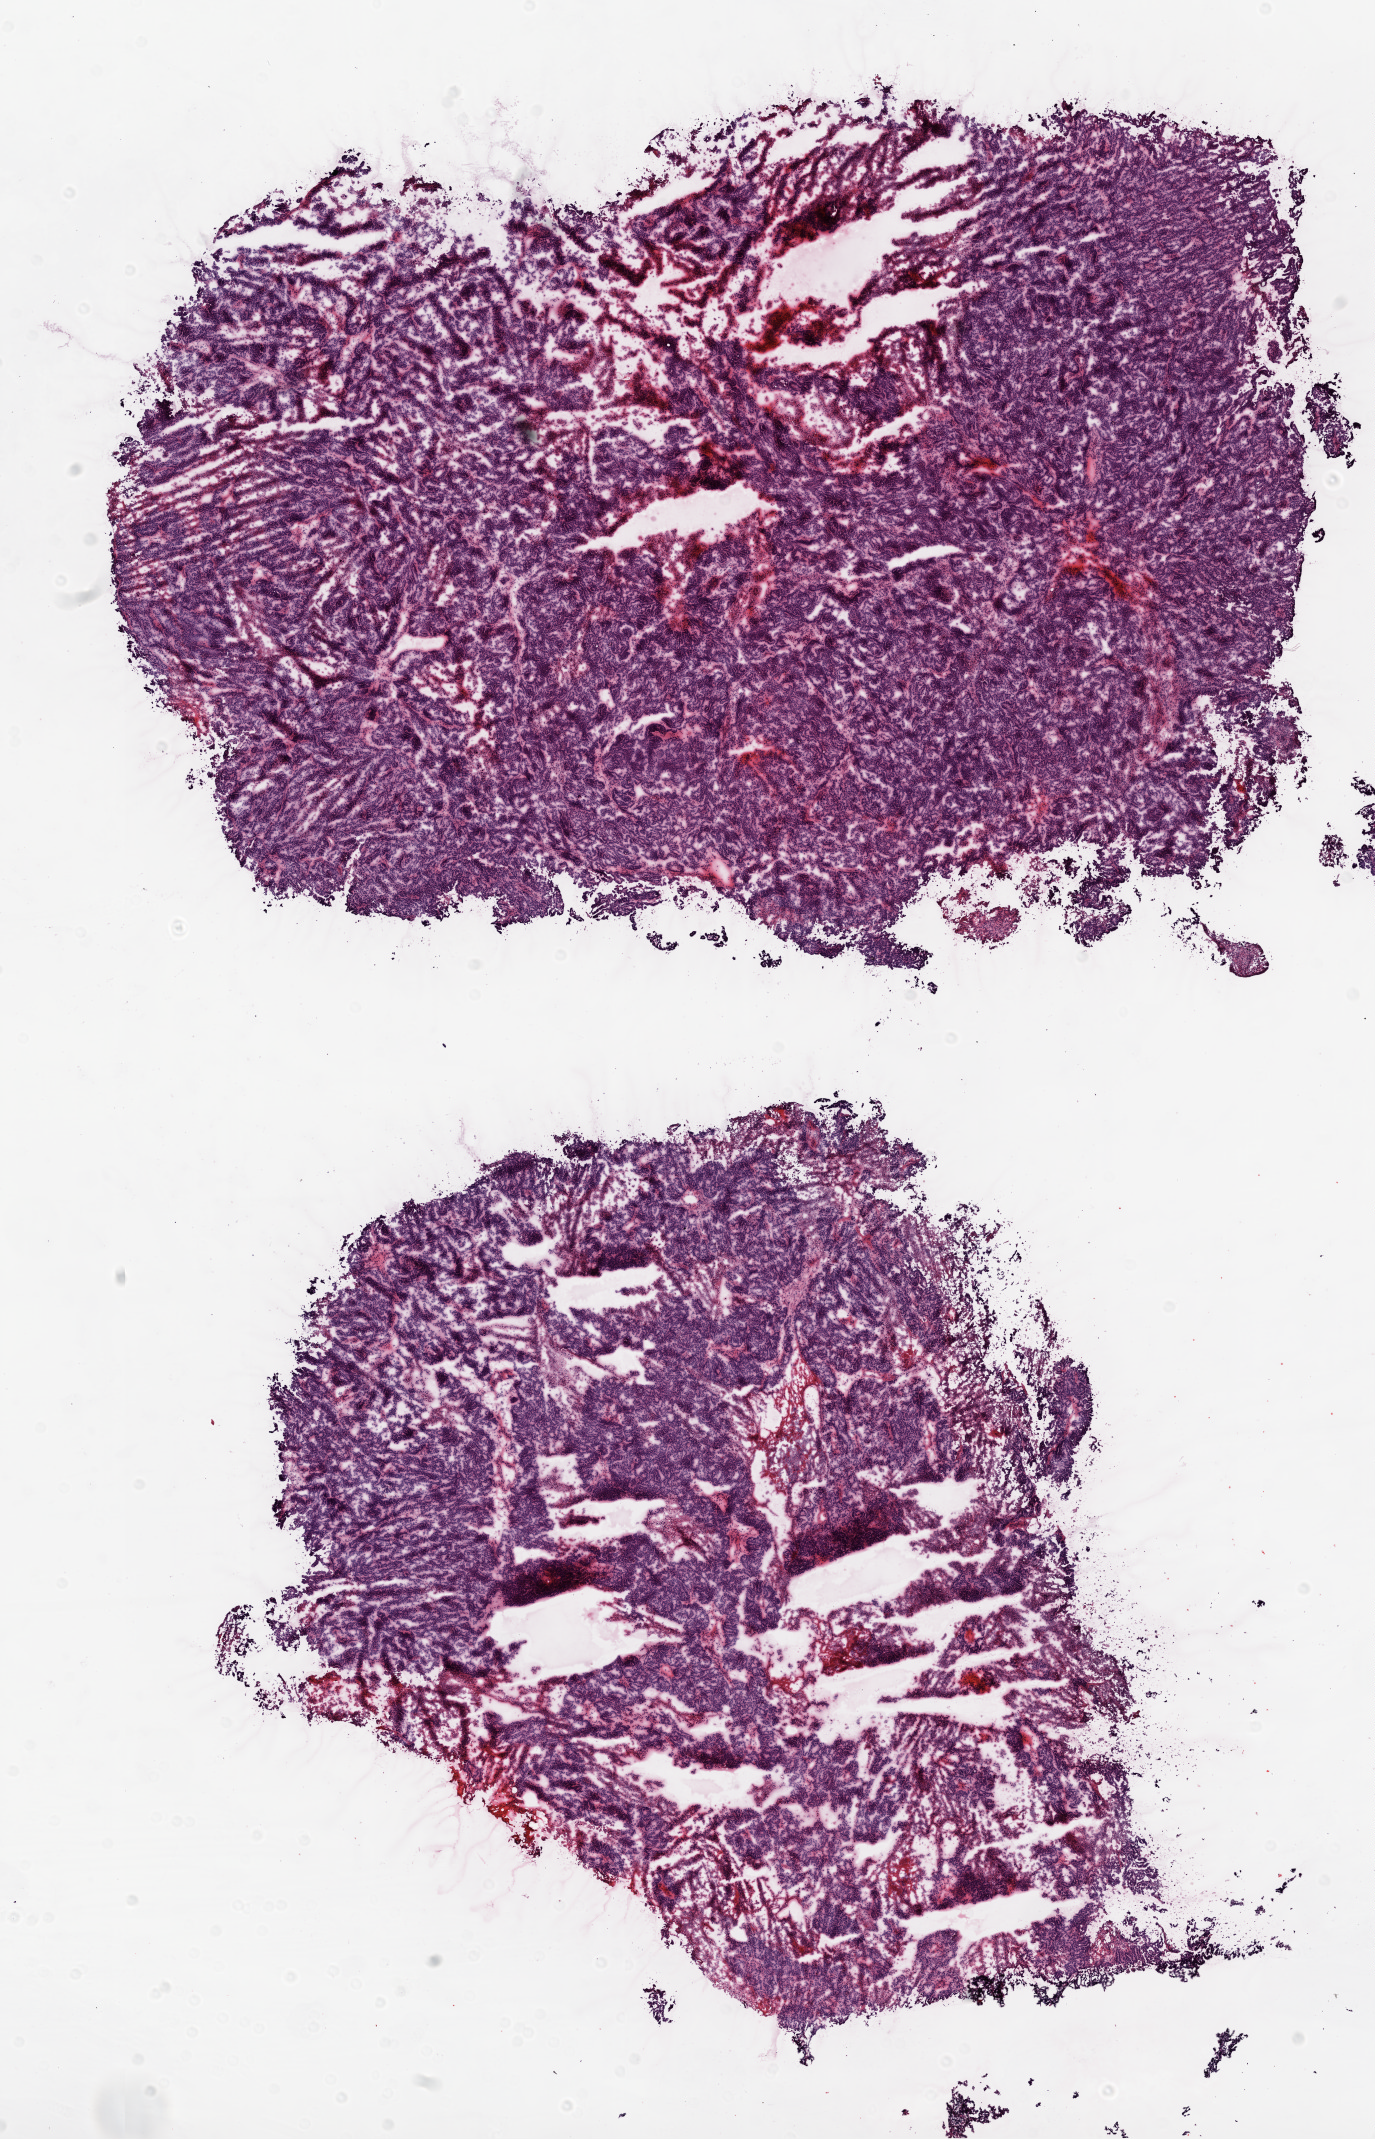
Digitized H&E tissue section (whole slide) — low-resolution overview of the scanned area, about 11.0 x 17.2 mm, frozen section from the top of the tissue portion, recurrent tumour sample from the ovary. Patient: female, age at initial diagnosis 70 years. Composition of this section per pathologist review: tumour cells 90%, tumour nuclei 95%, normal cells 0%, stromal cells 5%, necrosis 5%.
- this section: recurrent tumour
- patient diagnosis: Serous cystadenocarcinoma, NOS